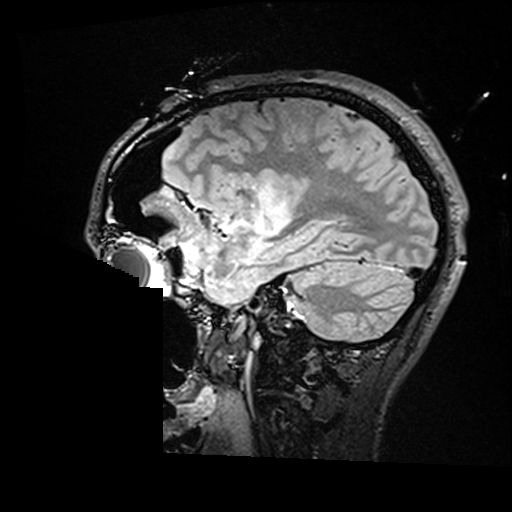
Brain MRI from a brain-tumour surgery series, one sagittal slice; slice 115 of 176 in the series (ordered by position); T2 FLAIR; 1 mm slice thickness; 512 × 512 image matrix. From the clinical record (not read from this slice): histopathology: Astrocytoma; WHO grade: 2; IDH mutation: yes; tumour location: Right Insular.
Outlined on this slice (outlined manually by an expert reader):
- residual tumour: bounding box (x1, y1, x2, y2) in pixels: (260, 186, 289, 230)